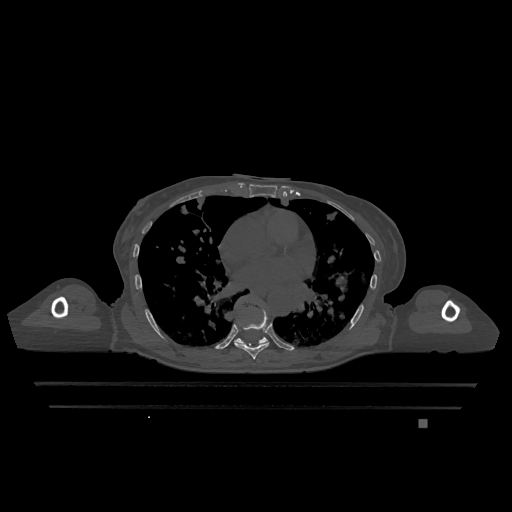
CT including the spine, one axial slice; position 723 of 1317 along the scan axis; bone window (W 1800 / L 400 HU); 0.5 mm slice thickness; 512 × 512 image matrix, field of view 500 × 500 mm. Patient: female, 74 years. Case-level facts recorded for this patient, not image findings: primary cancer: lung.
Structures marked on this image (semi-automatic segmentation, software-assisted and operator-edited):
- T7 vertebra: bounding box [x1, y1, x2, y2] px = [234, 310, 270, 360]
- T9 vertebra: [234, 309, 268, 345]